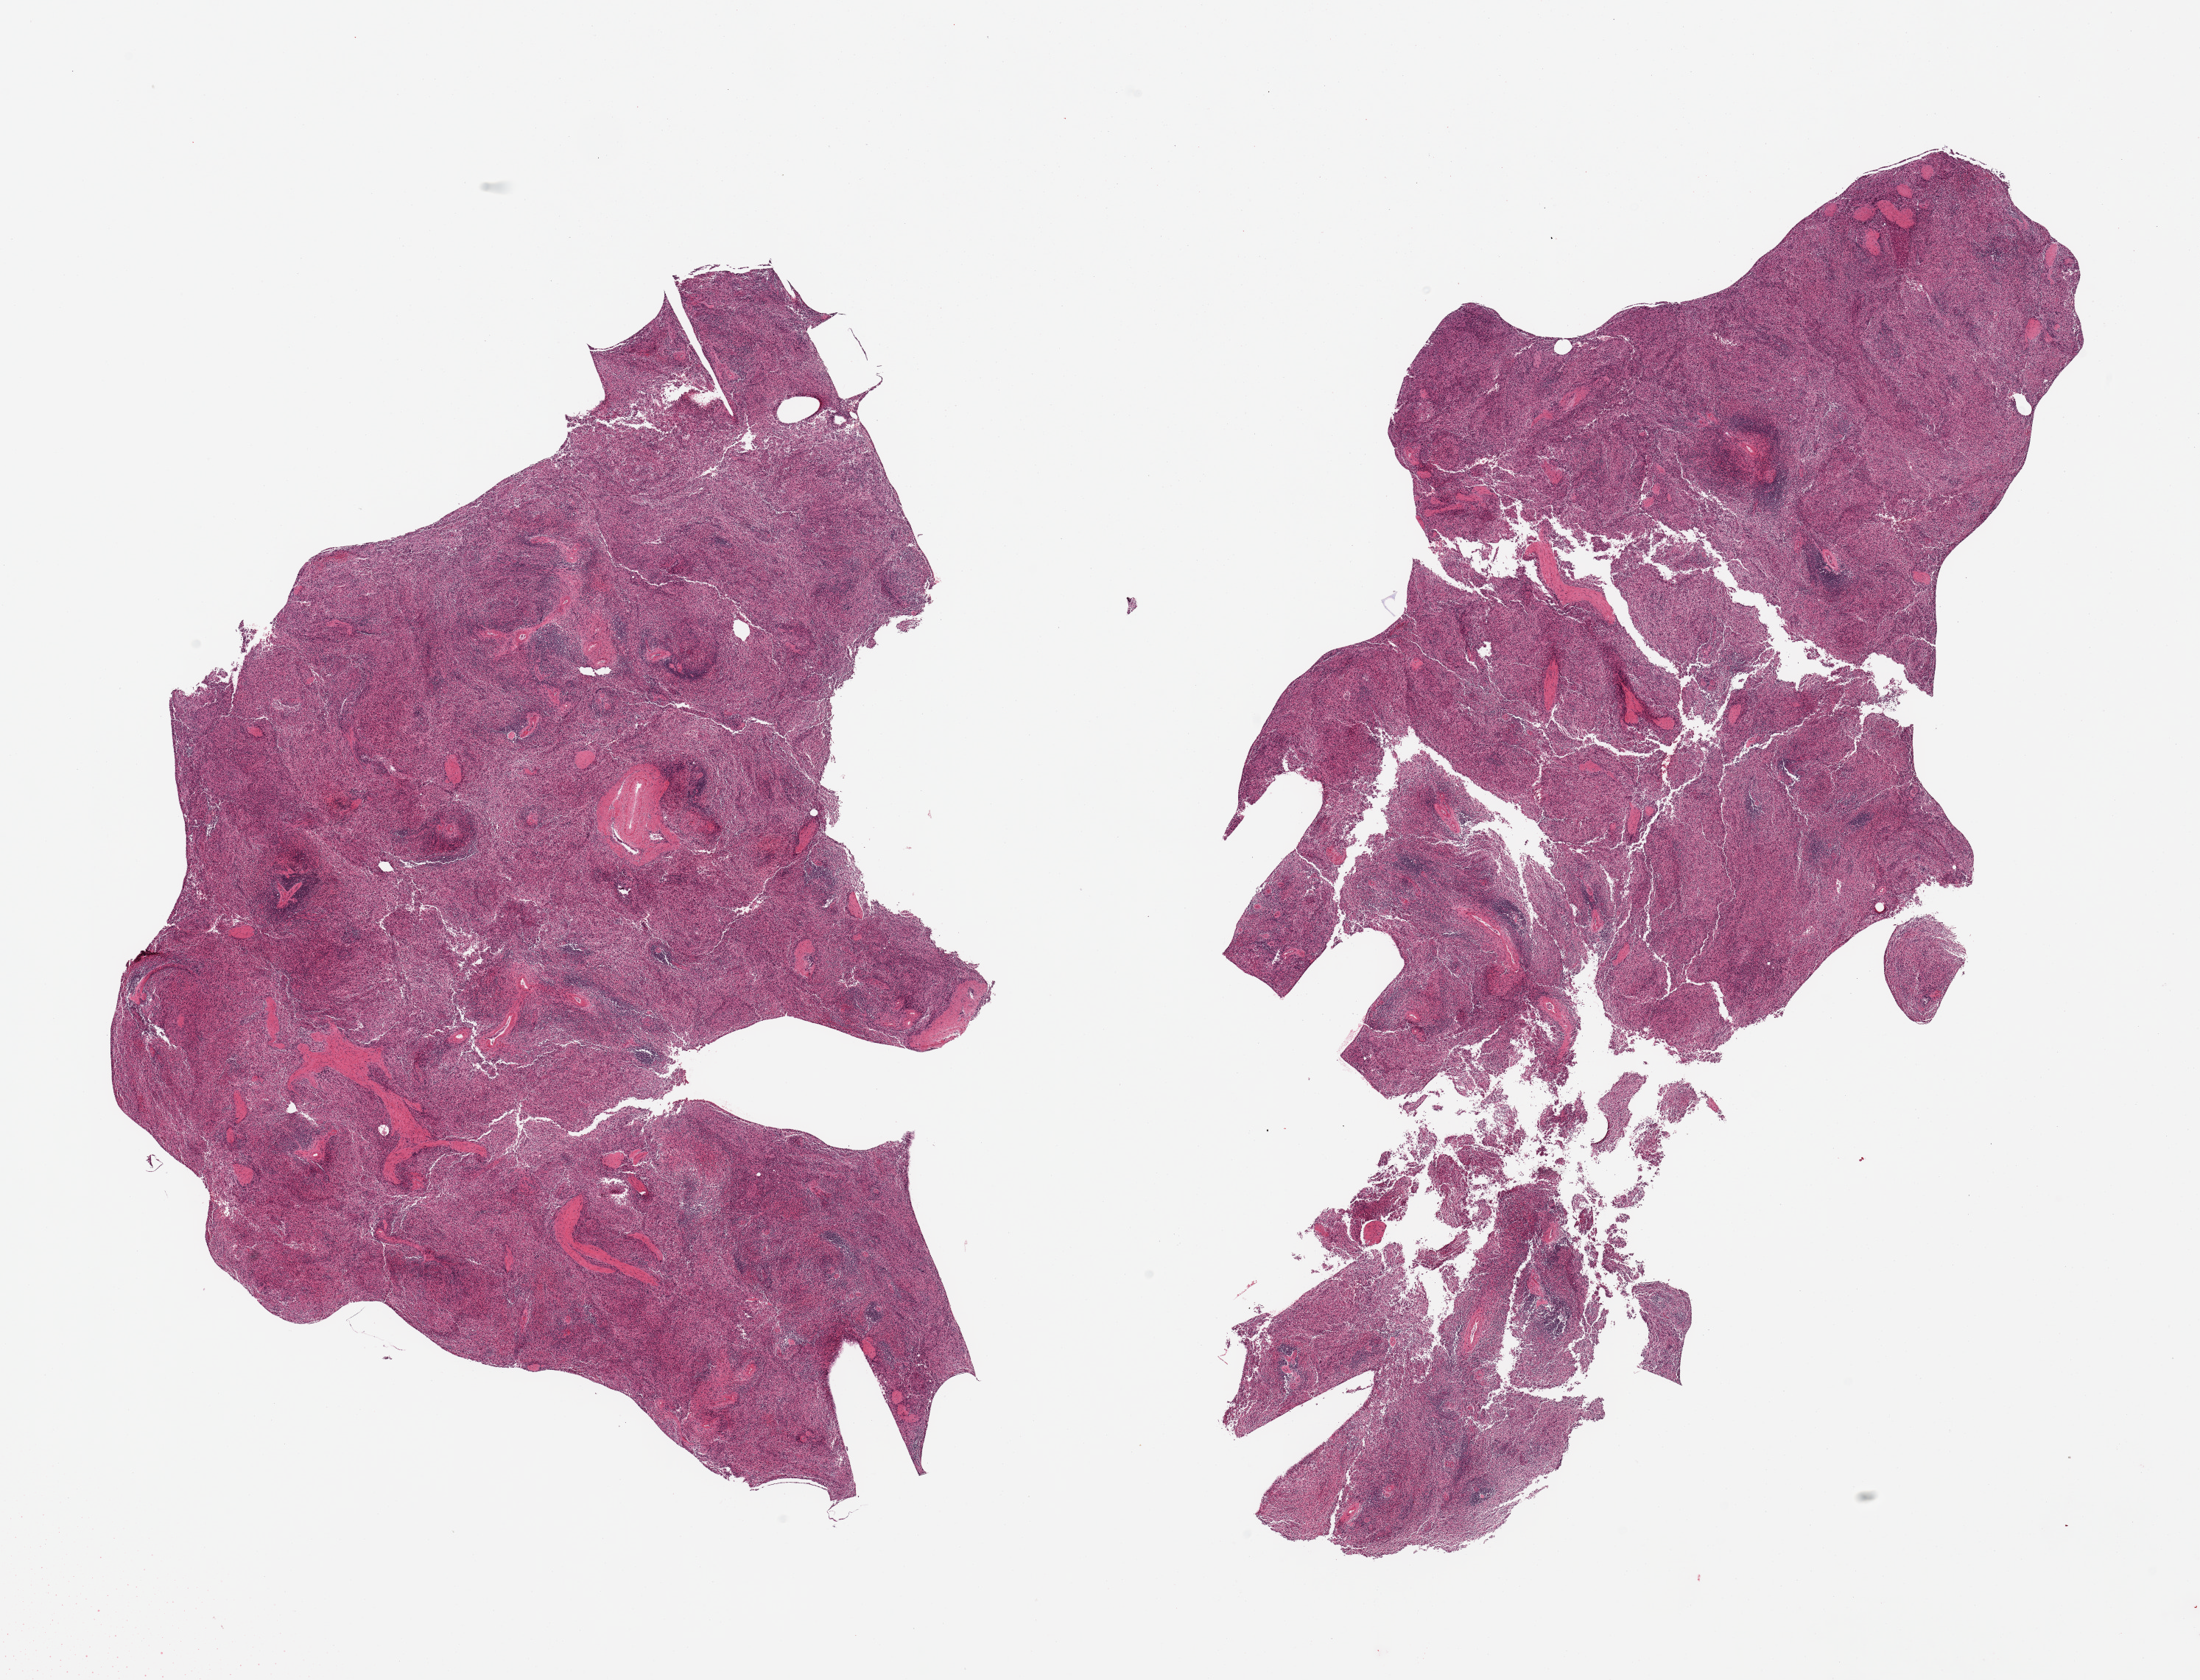
Haematoxylin and eosin whole-slide image, brightfield — low-resolution overview of the scanned area, about 23.6 x 18.0 mm; PAXgene-fixed, paraffin-embedded tissue; sampled site (target tissue): spleen; tissue donor sample. Male donor.
Review note (as recorded): 2 pieces; one piece fragmented.